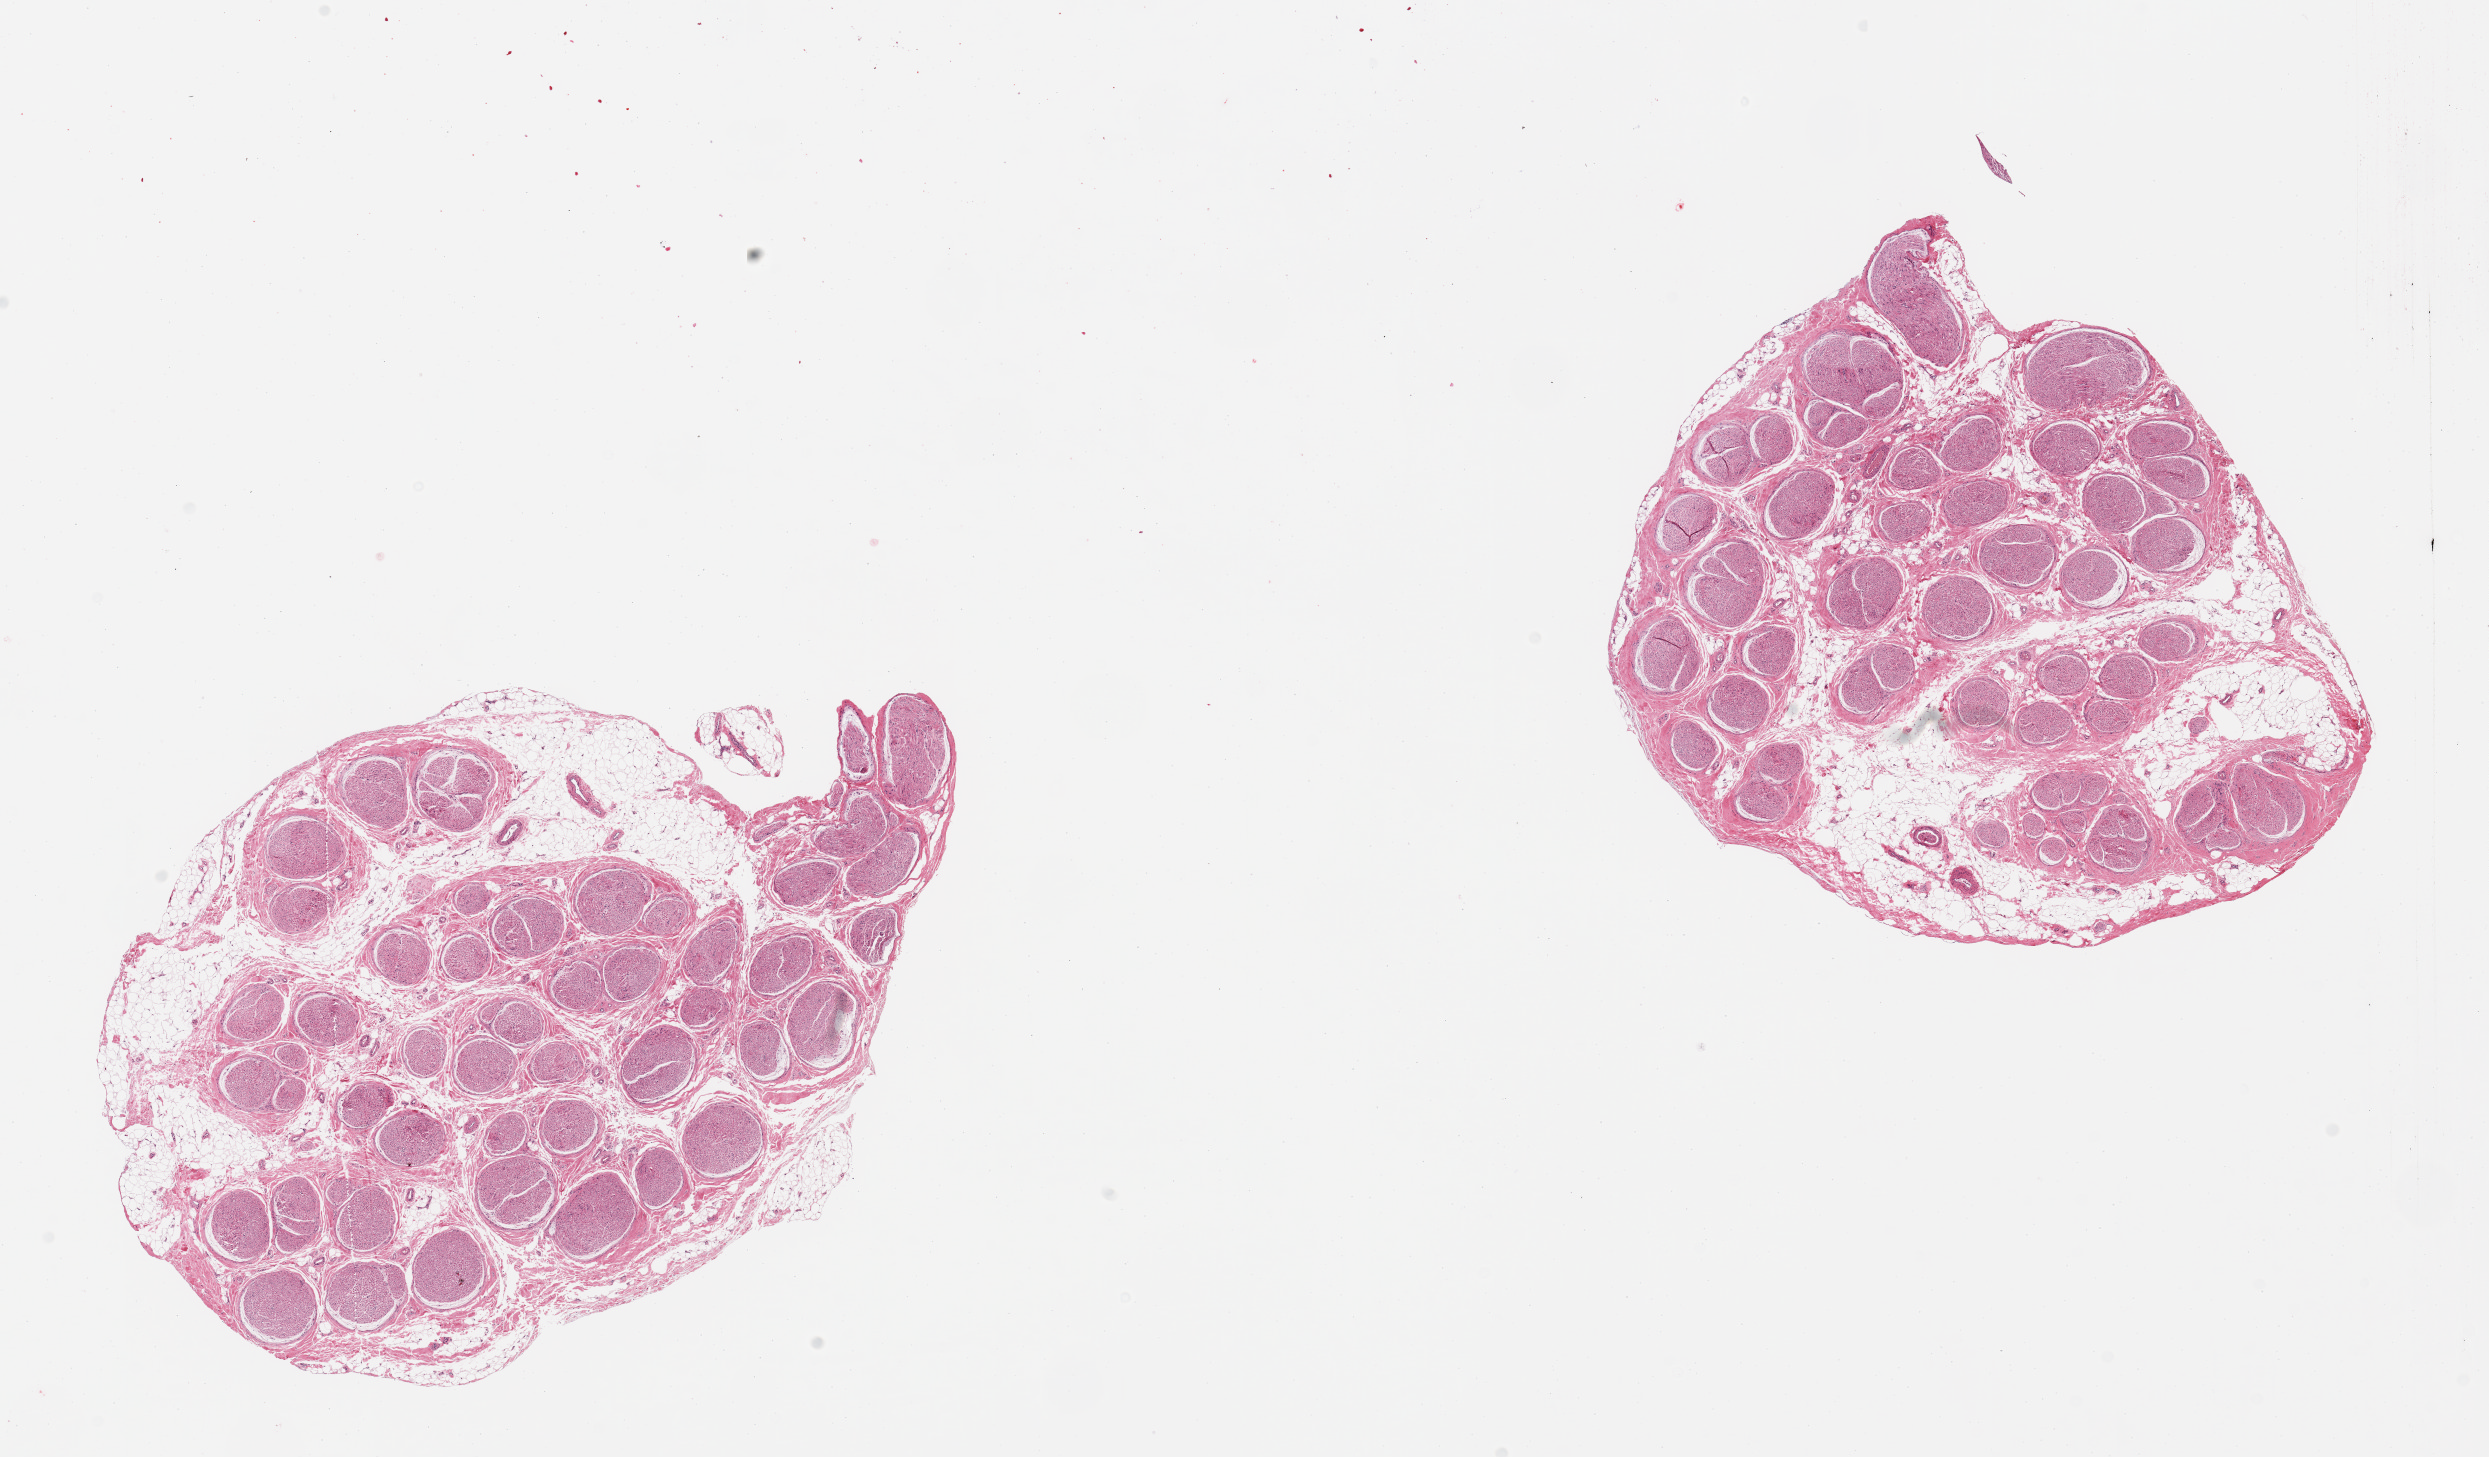
Whole-slide image, haematoxylin and eosin stain — whole scanned area (about 19.7 x 11.5 mm, slide scanned at 20x) shown as a low-resolution overview, PAXgene-fixed paraffin-embedded (PFPE) section, sampled site (target tissue): tibial nerve, tissue donor sample. Donor sex: male.
* pathologist's review note for this sample: 2 pieces, clean specimens